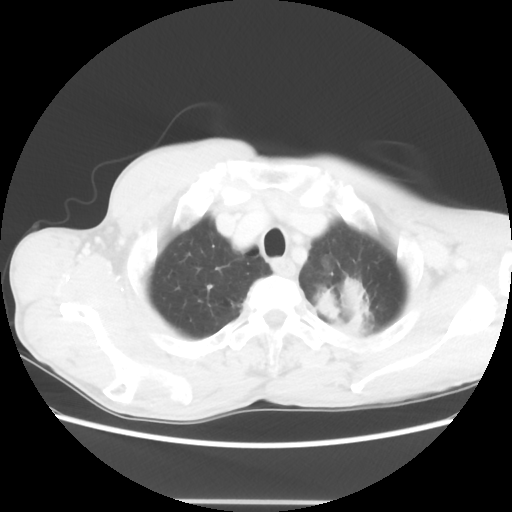
Chest CT, one axial slice. Position 57 of 62 along the scan axis. Reconstruction kernel STANDARD. Lung window (W 1500 / L -600 HU). 5 mm slice thickness. 512 × 512 image matrix, field of view 360 × 360 mm. Male patient, age 61 years. Case-level facts recorded for this patient, not image findings: clinical TNM (as recorded): T3 N1 M1.
Structures marked on this image (rectangle marked by the reading radiologist):
- lung tumour (recorded histology: adenocarcinoma): bounding box <312,275,385,348> (left, top, right, bottom; pixels)